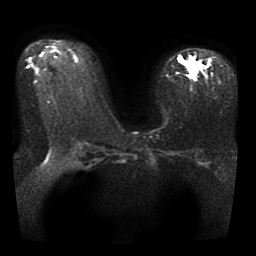
Breast MRI, one axial slice; diffusion-weighted series; image 2 of 4 stored at this slice position (different b-values; order by instance number); 1.5 T; 5 mm slice thickness; 256 × 256 image matrix, field of view 330 × 330 mm. Female patient.
Structures marked on this image (manually delineated by an expert):
- tumour on diffusion-weighted imaging: bounding box (x1, y1, x2, y2) in pixels: (178, 56, 200, 75)